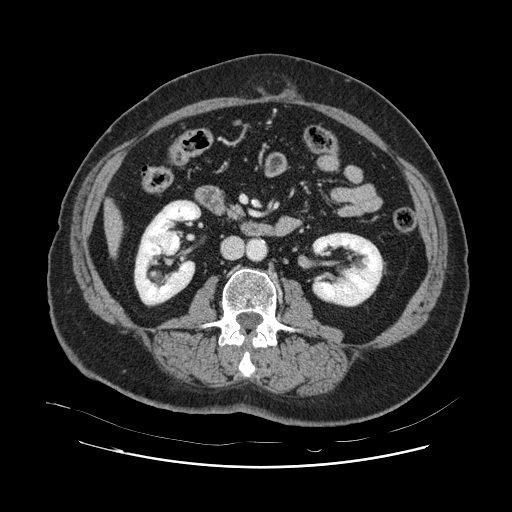
Contrast-enhanced abdominal CT, one axial slice; position 21 of 132 along the scan axis; 120 kVp; intravenous contrast given; soft-tissue window (W 400 / L 40 HU); 512 × 512 image matrix, field of view 391 × 391 mm. Female patient, age 73 years. From the clinical record (not read from this slice): diagnosis: colorectal cancer liver metastases, imaged before liver resection; multiple liver metastases: no; largest metastasis: 7 cm; chemotherapy before resection: yes.
Structures marked on this image (outlined manually by an expert reader):
- liver: bounding box <106,205,121,250> (left, top, right, bottom; pixels)
- planned liver remnant (the part of the liver to remain after resection): <106,205,121,251>